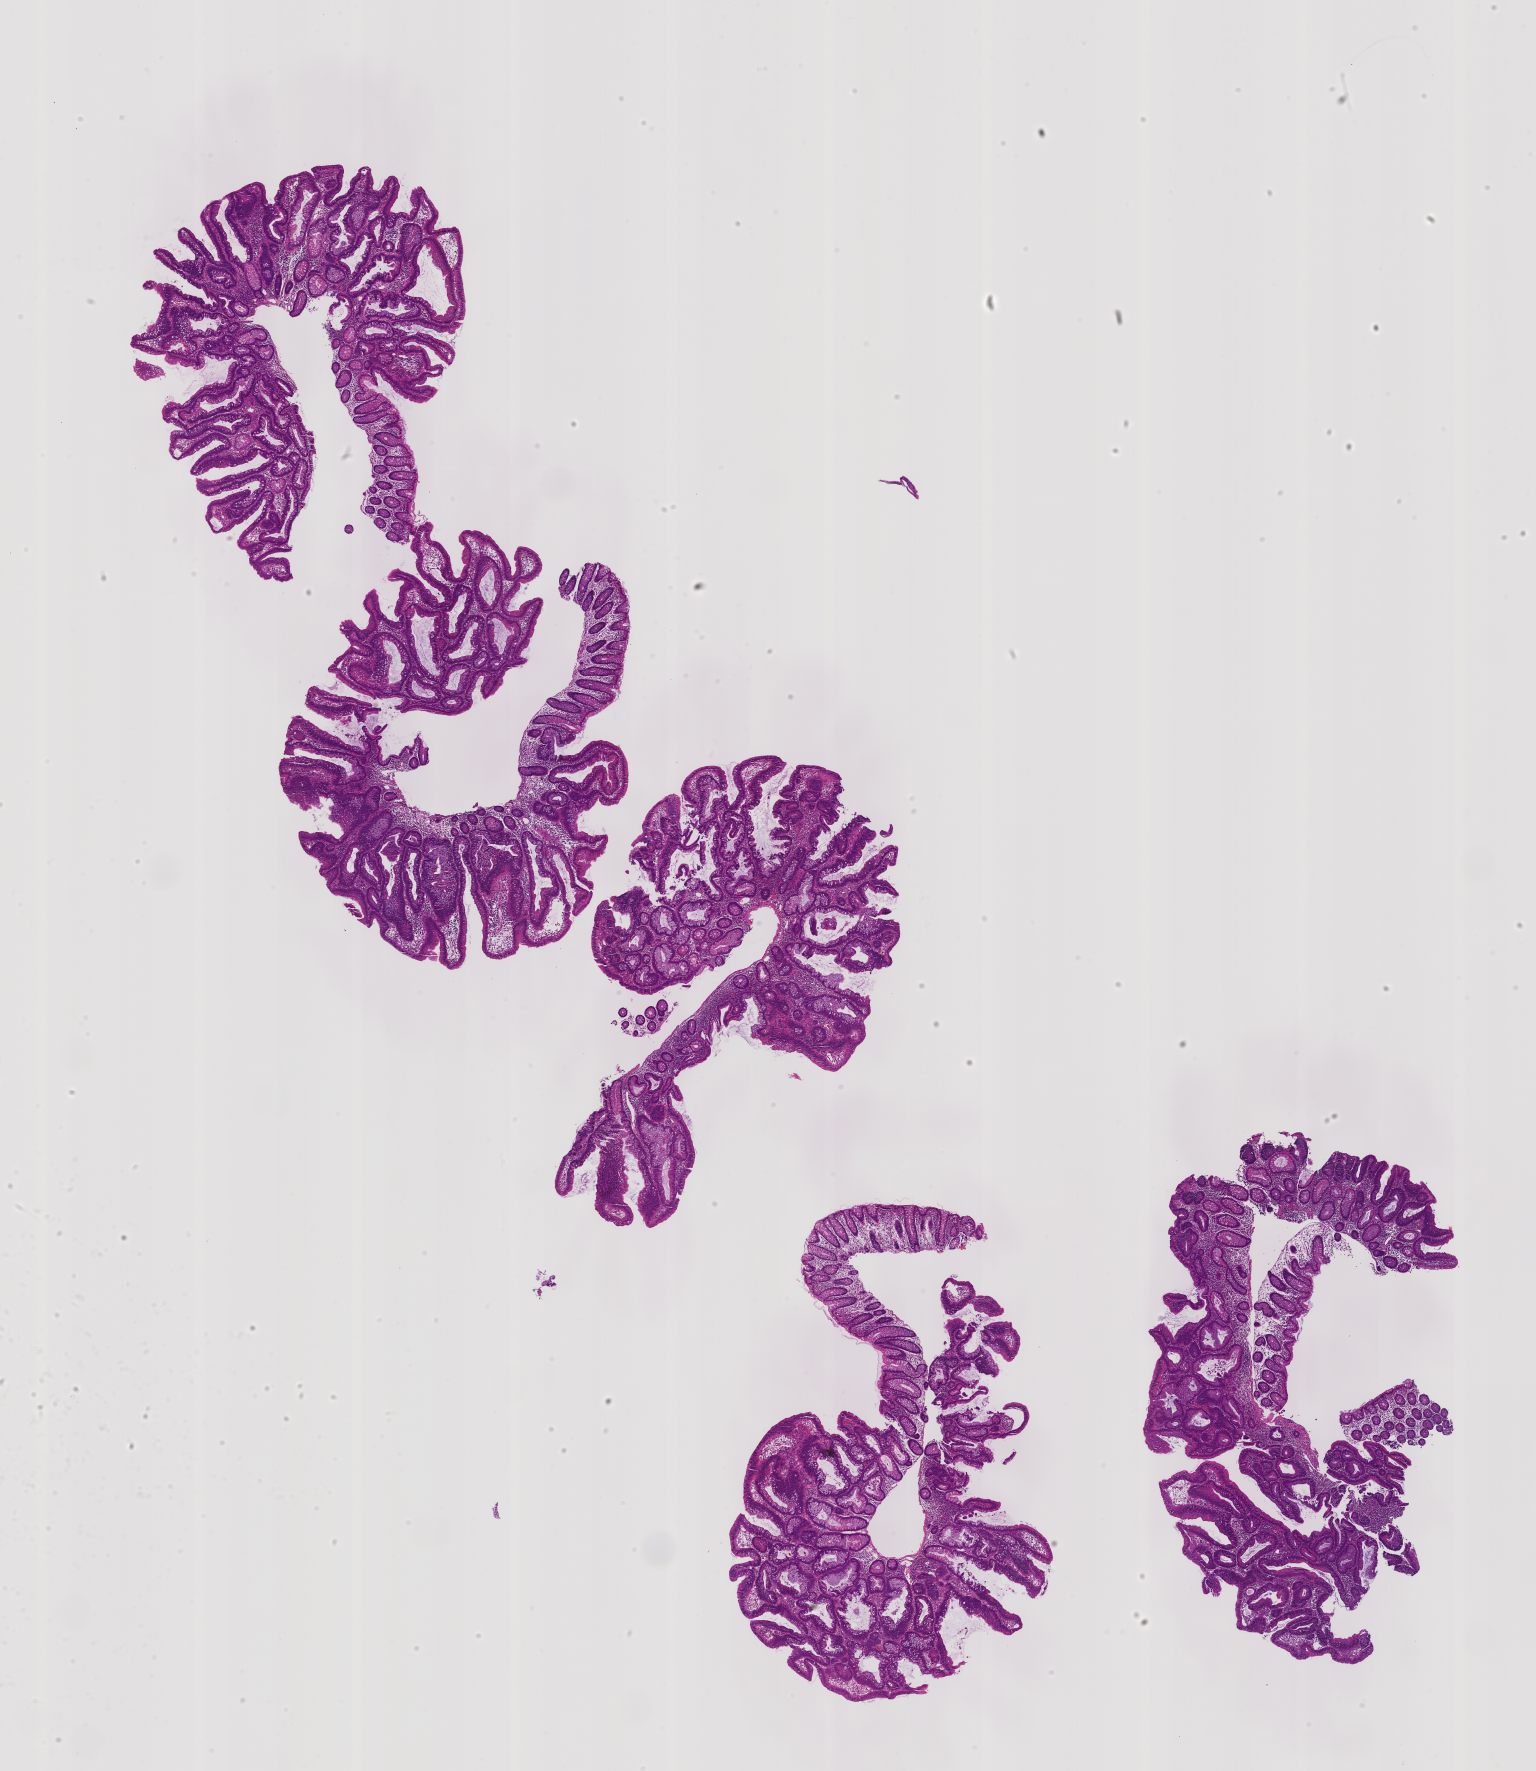
H&E whole-slide image of a colon biopsy, a low-resolution overview of the entire scanned area, about 12.3 x 14.2 mm. Formalin-fixed paraffin-embedded section. Cecum. Female patient.
Lesion category (as recorded): premalignant.